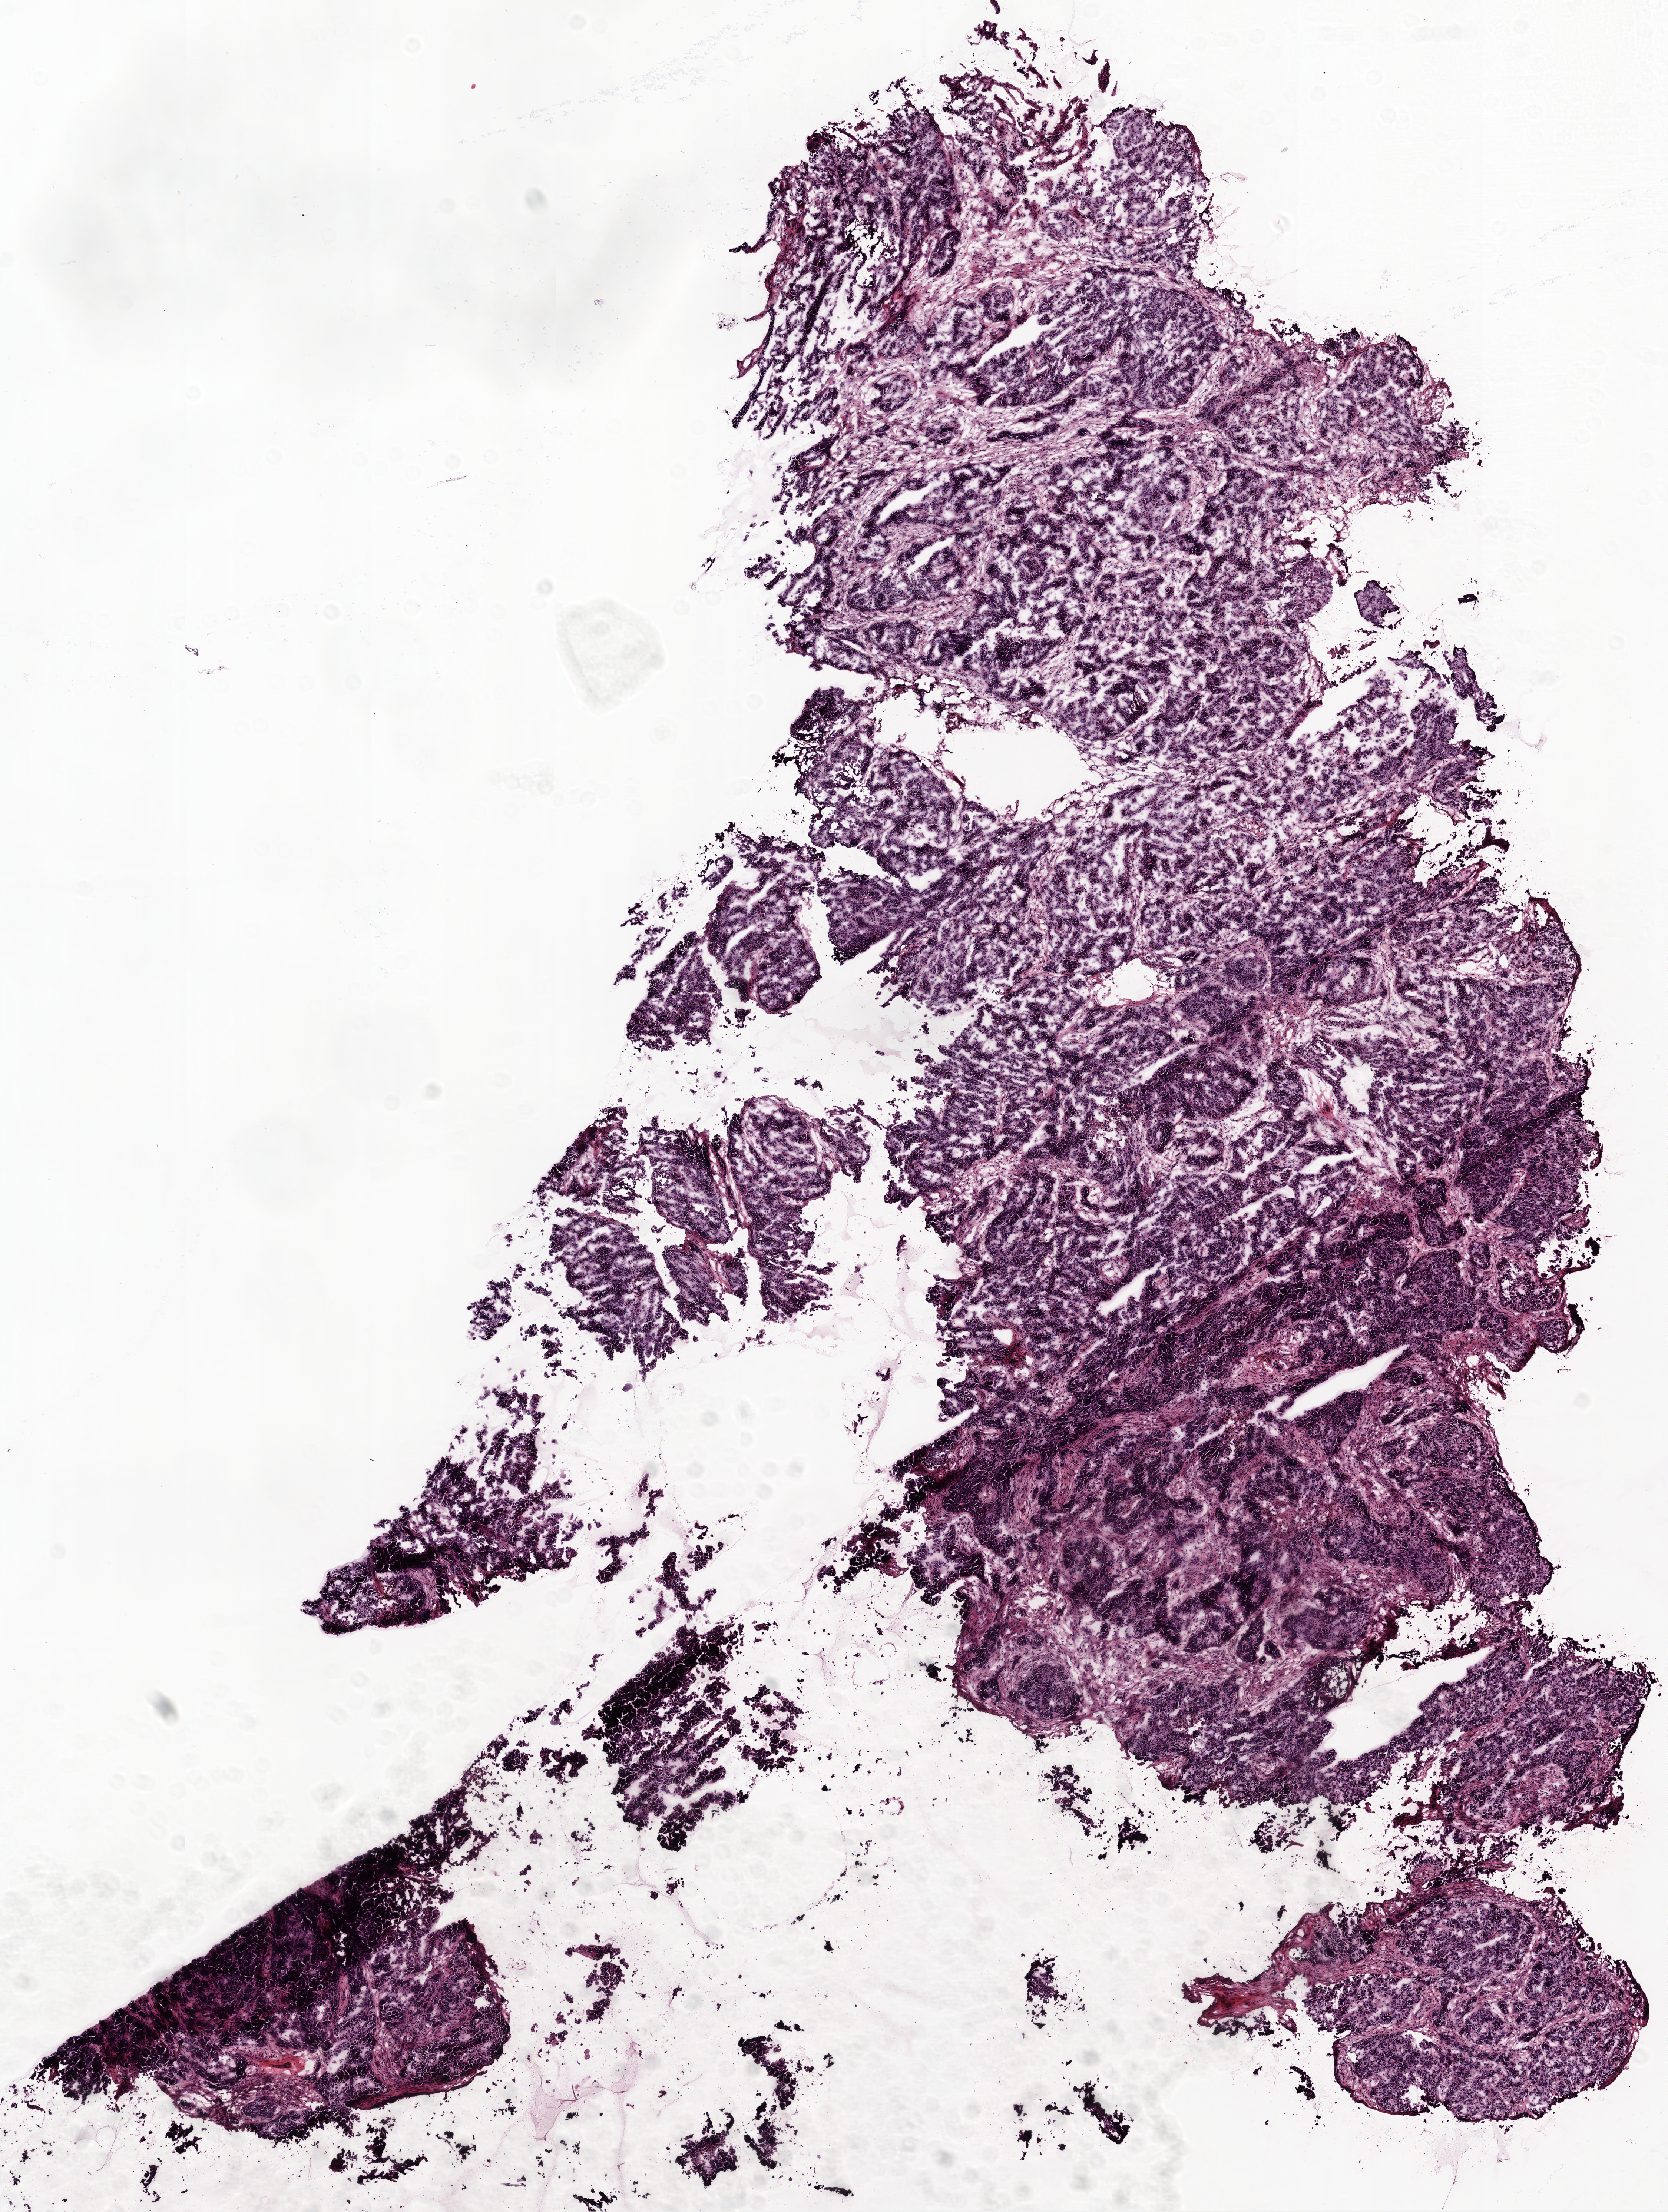
Whole-slide histology image, H&E-stained — whole scanned area (about 9.0 x 12.0 mm) shown as a low-resolution overview, frozen section from the top of the tissue portion, ovary, primary tumour sample. Female patient; age at initial diagnosis 39 years. Pathologist review of this section (percent, as recorded): tumour cells 100%, tumour nuclei 70%.
Diagnosis: Serous cystadenocarcinoma, NOS.